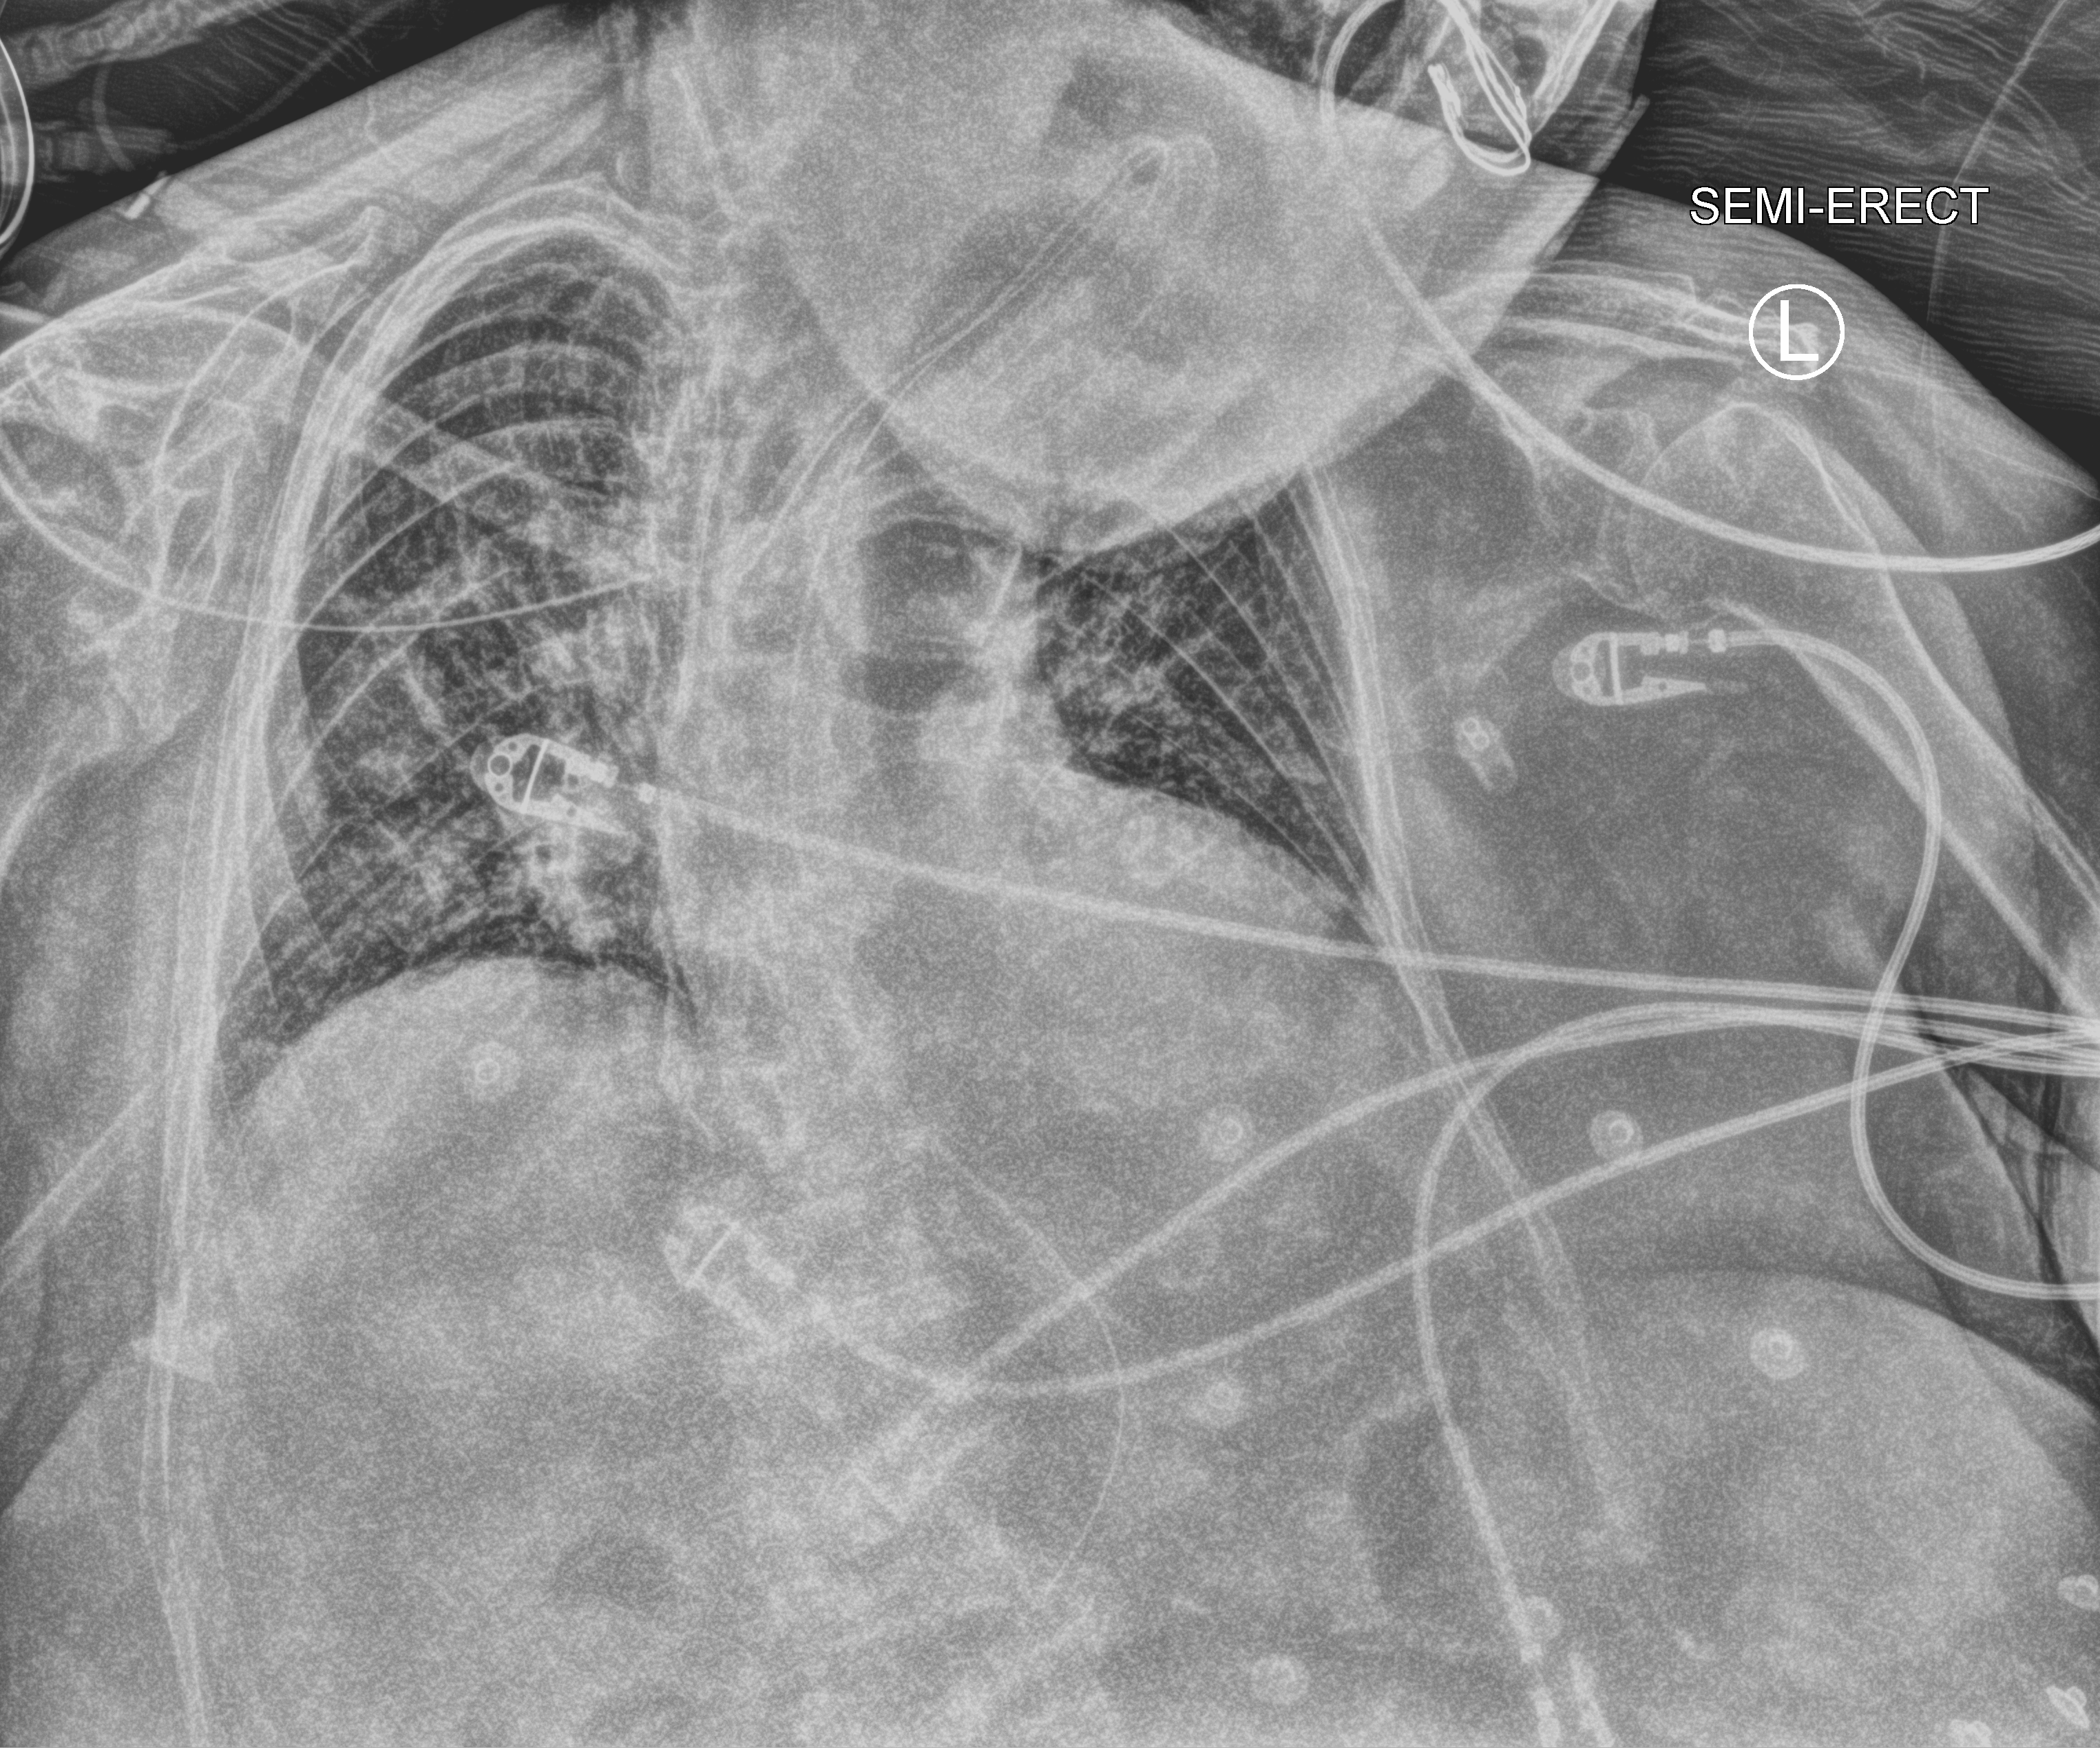
Bedside chest radiograph (computed radiography). Female patient hospitalised with COVID-19, age 75–90 years.
Hospital-stay facts (about this admission, not read from this image; timing relative to this image not recorded):
- admitted to intensive care during this hospital stay: yes